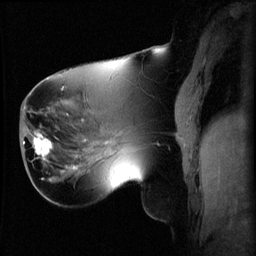
Breast MRI (dynamic contrast-enhanced), one sagittal slice. Slice 25 of 60 in the series (ordered by position). 3 images stored at this slice position (order not interpretable as contrast timing). 1.5 T. TE 4.2 ms, TR 8.2 ms. 2.2 mm slice thickness. 256 × 256 image matrix, field of view 220 × 220 mm. Patient: female, 62 years.
Annotated regions visible in this slice (semi-automatic segmentation, software-assisted and operator-edited):
- analysis volume of interest (the breast-tissue region the enhancement analysis was run in; not a lesion): bounding box <26,126,59,165> (left, top, right, bottom; pixels)
- tumour enhancement mask (voxels above the 70 % enhancement threshold inside the analysis volume of interest): <34,132,53,157>